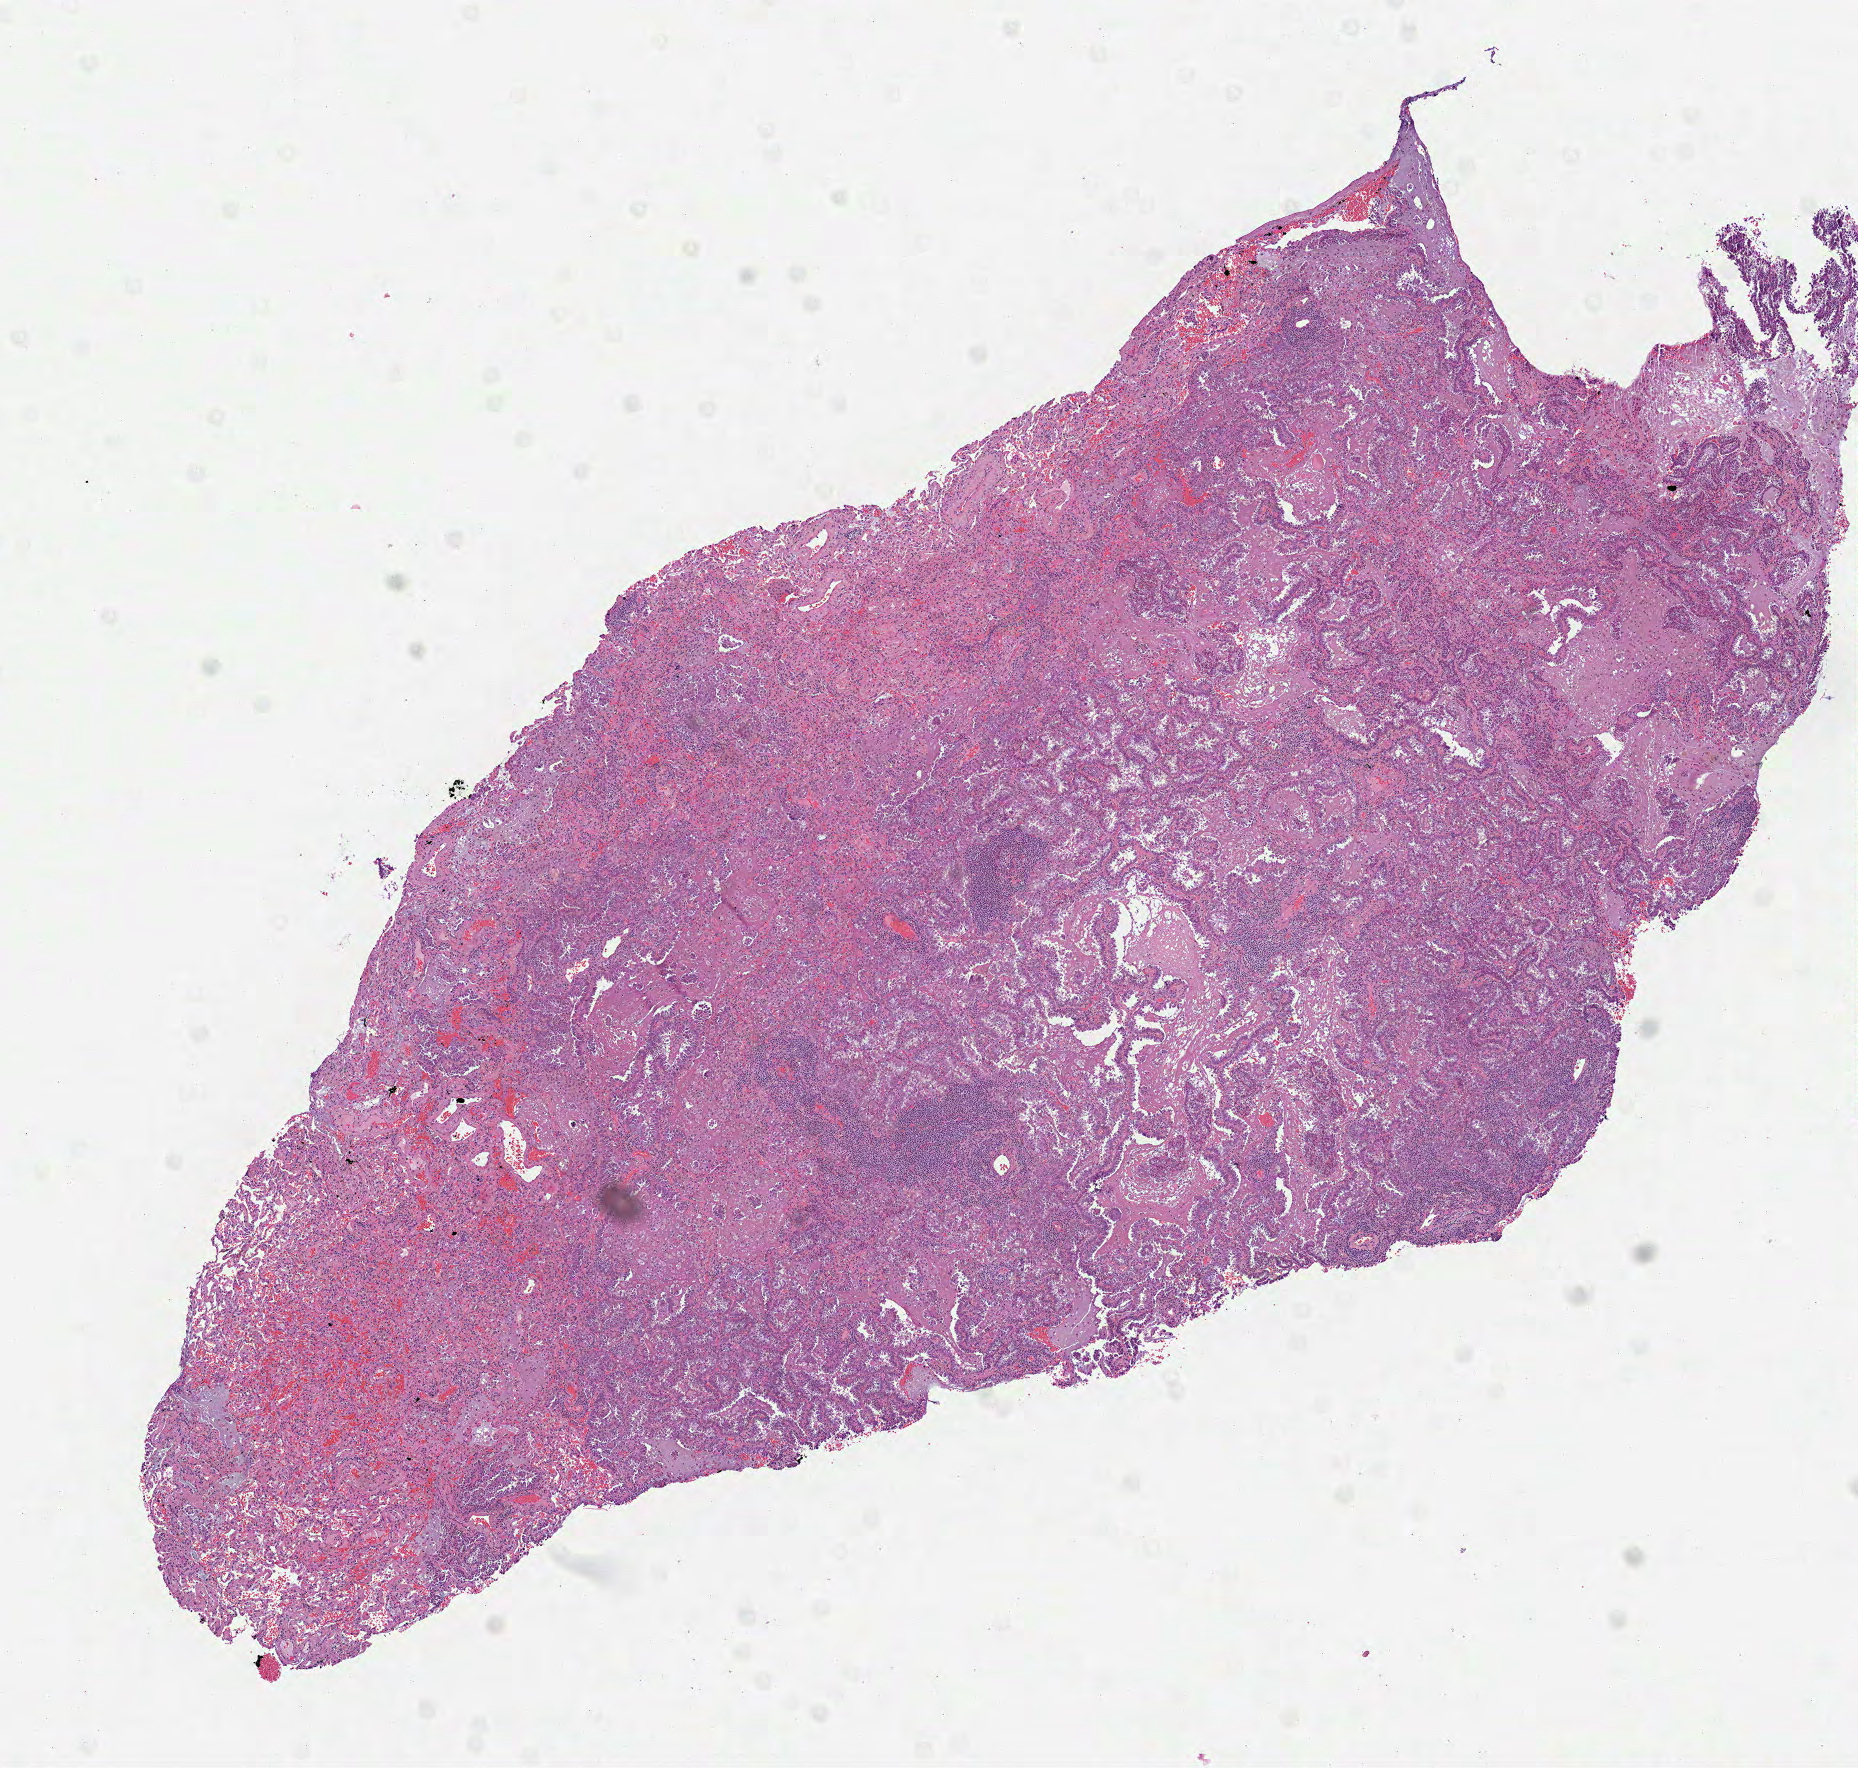
Whole-slide histology image, H&E-stained, whole scanned area (about 7.5 x 7.1 mm, slide scanned at 40x) shown as a low-resolution overview; FFPE section; primary tumour sample from the lung. Patient: female, age at initial diagnosis 68 years.
Diagnosis: Adenocarcinoma, NOS. Laterality: right. AJCC pathologic stage: IA.